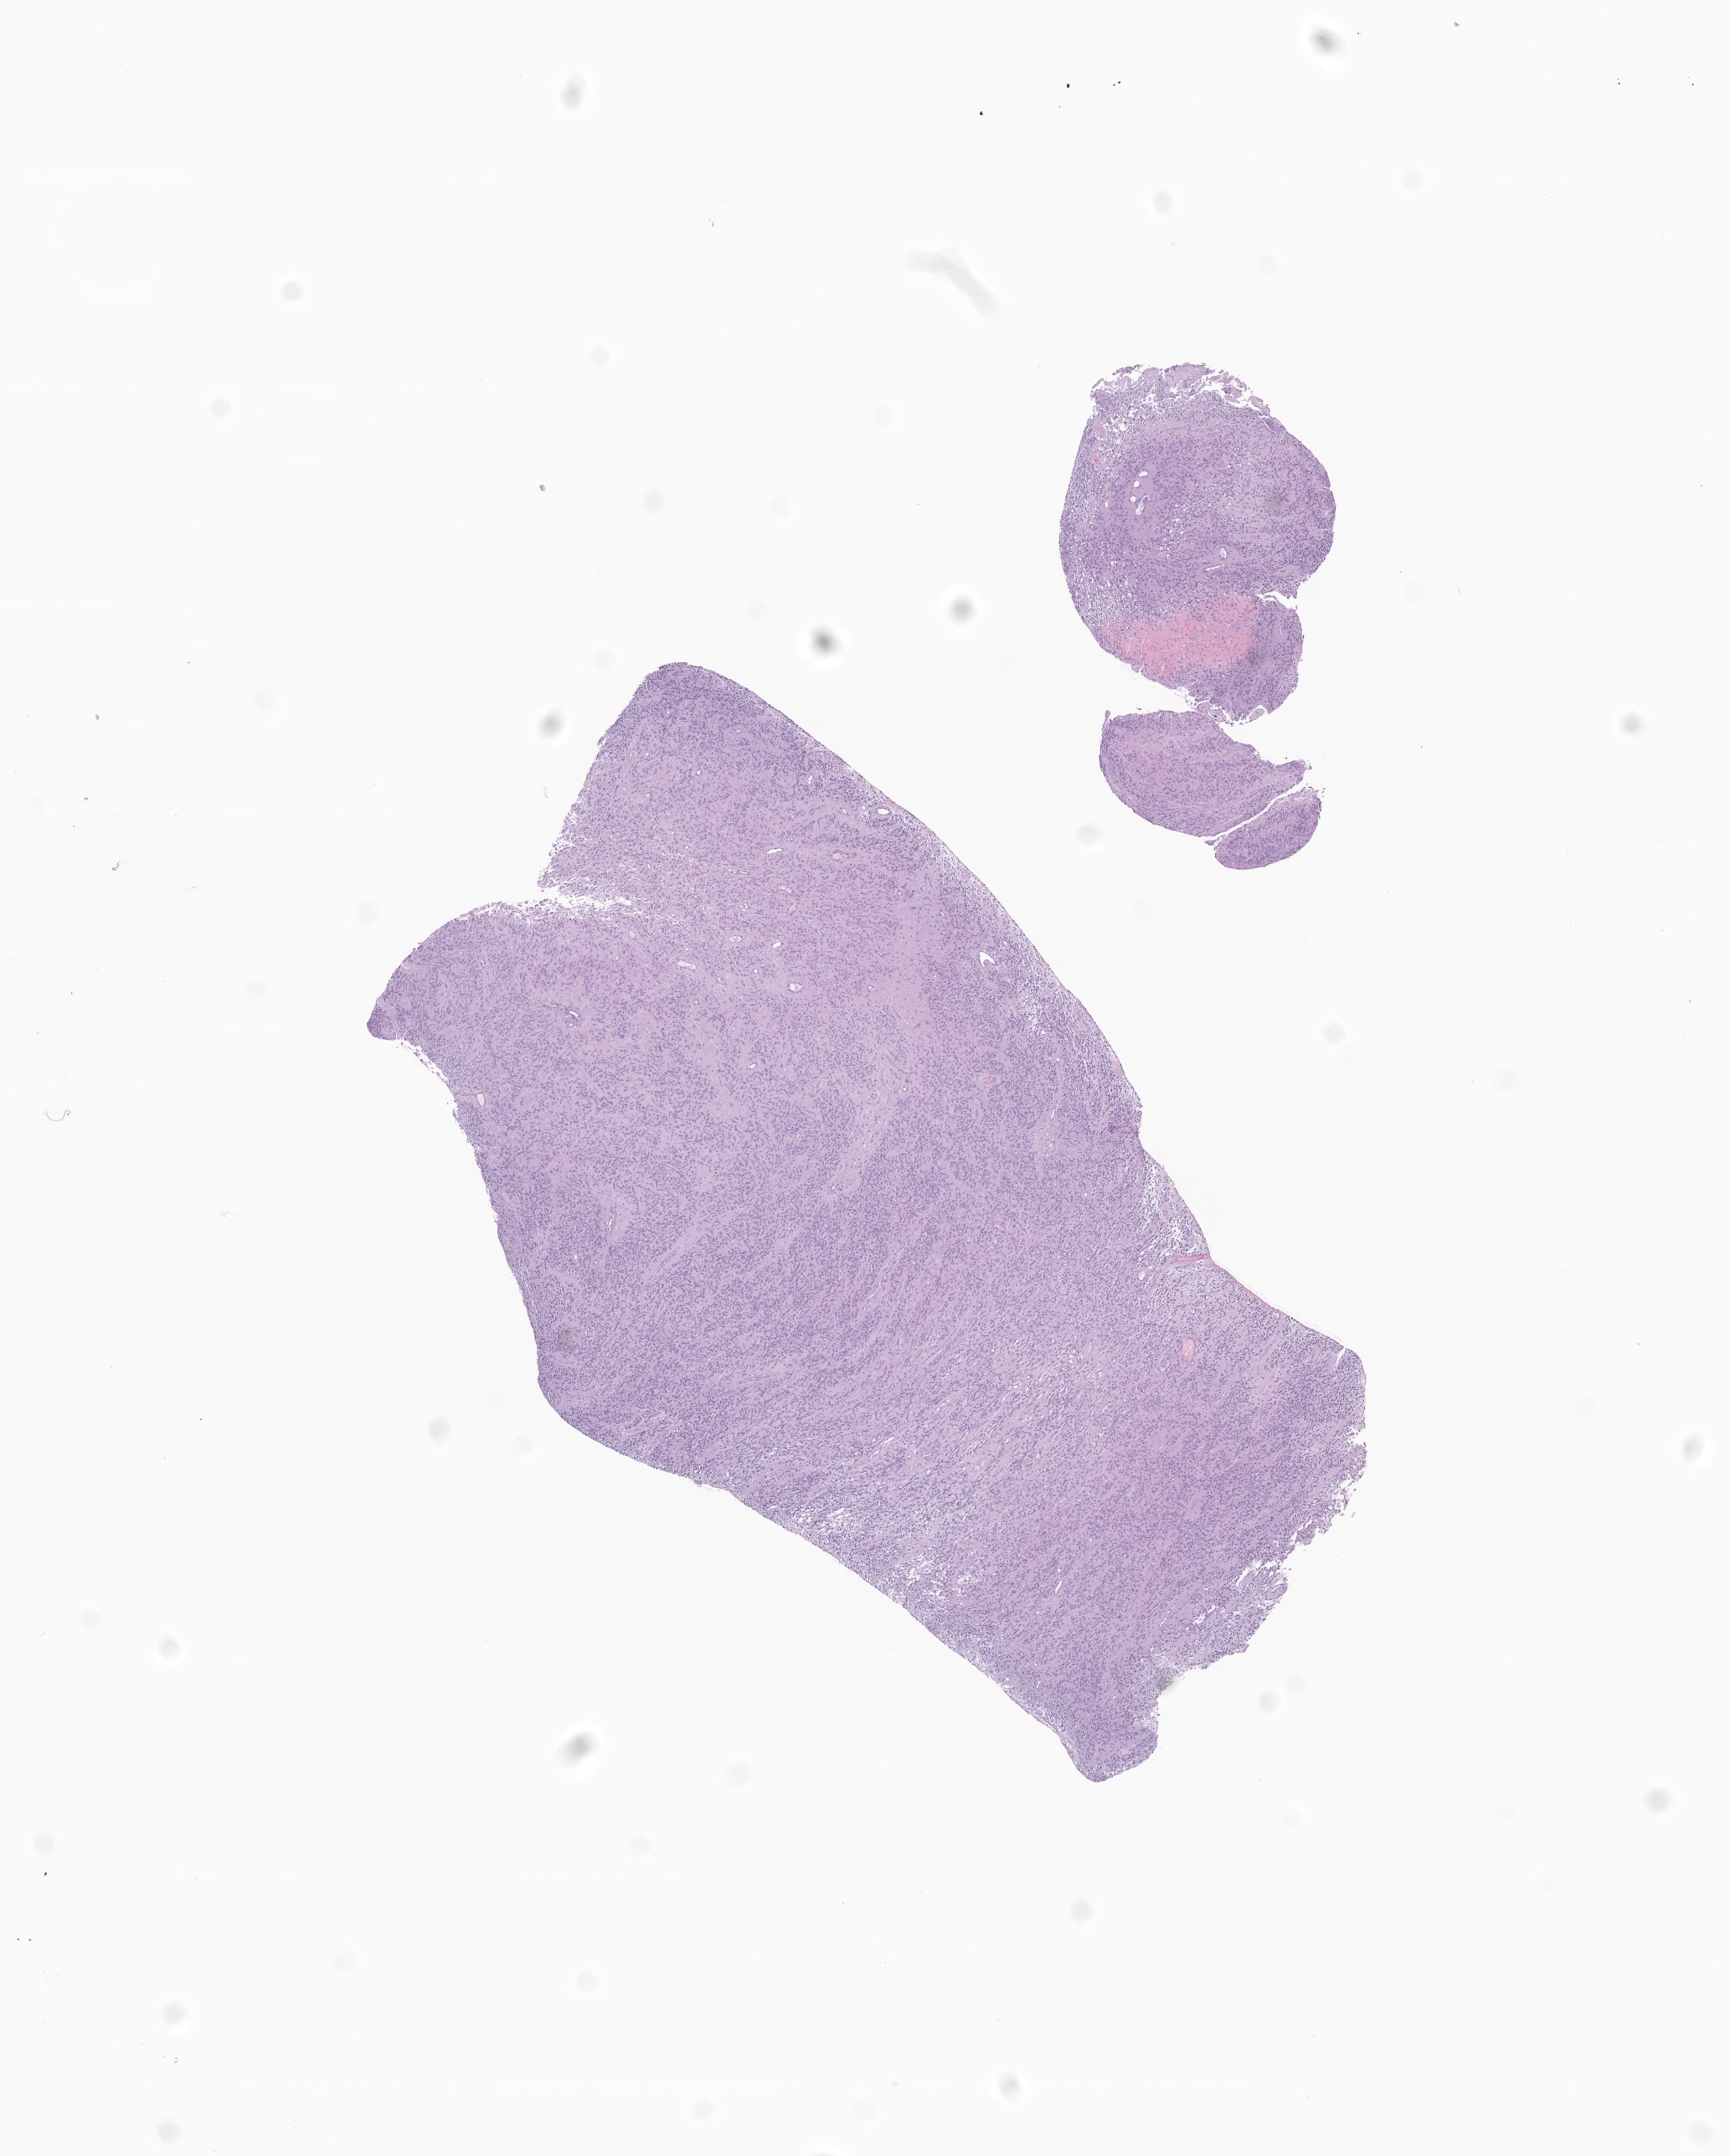
Digitized haematoxylin and eosin-stained section of tumor tissue from the brain, whole scanned area (about 8.7 x 10.9 mm) shown as a low-resolution overview, formalin-fixed, paraffin-embedded (FFPE) tissue. Patient male; age 782 days.
Diagnosis (ICD-O-3 morphology term): Ependymoma, NOS.